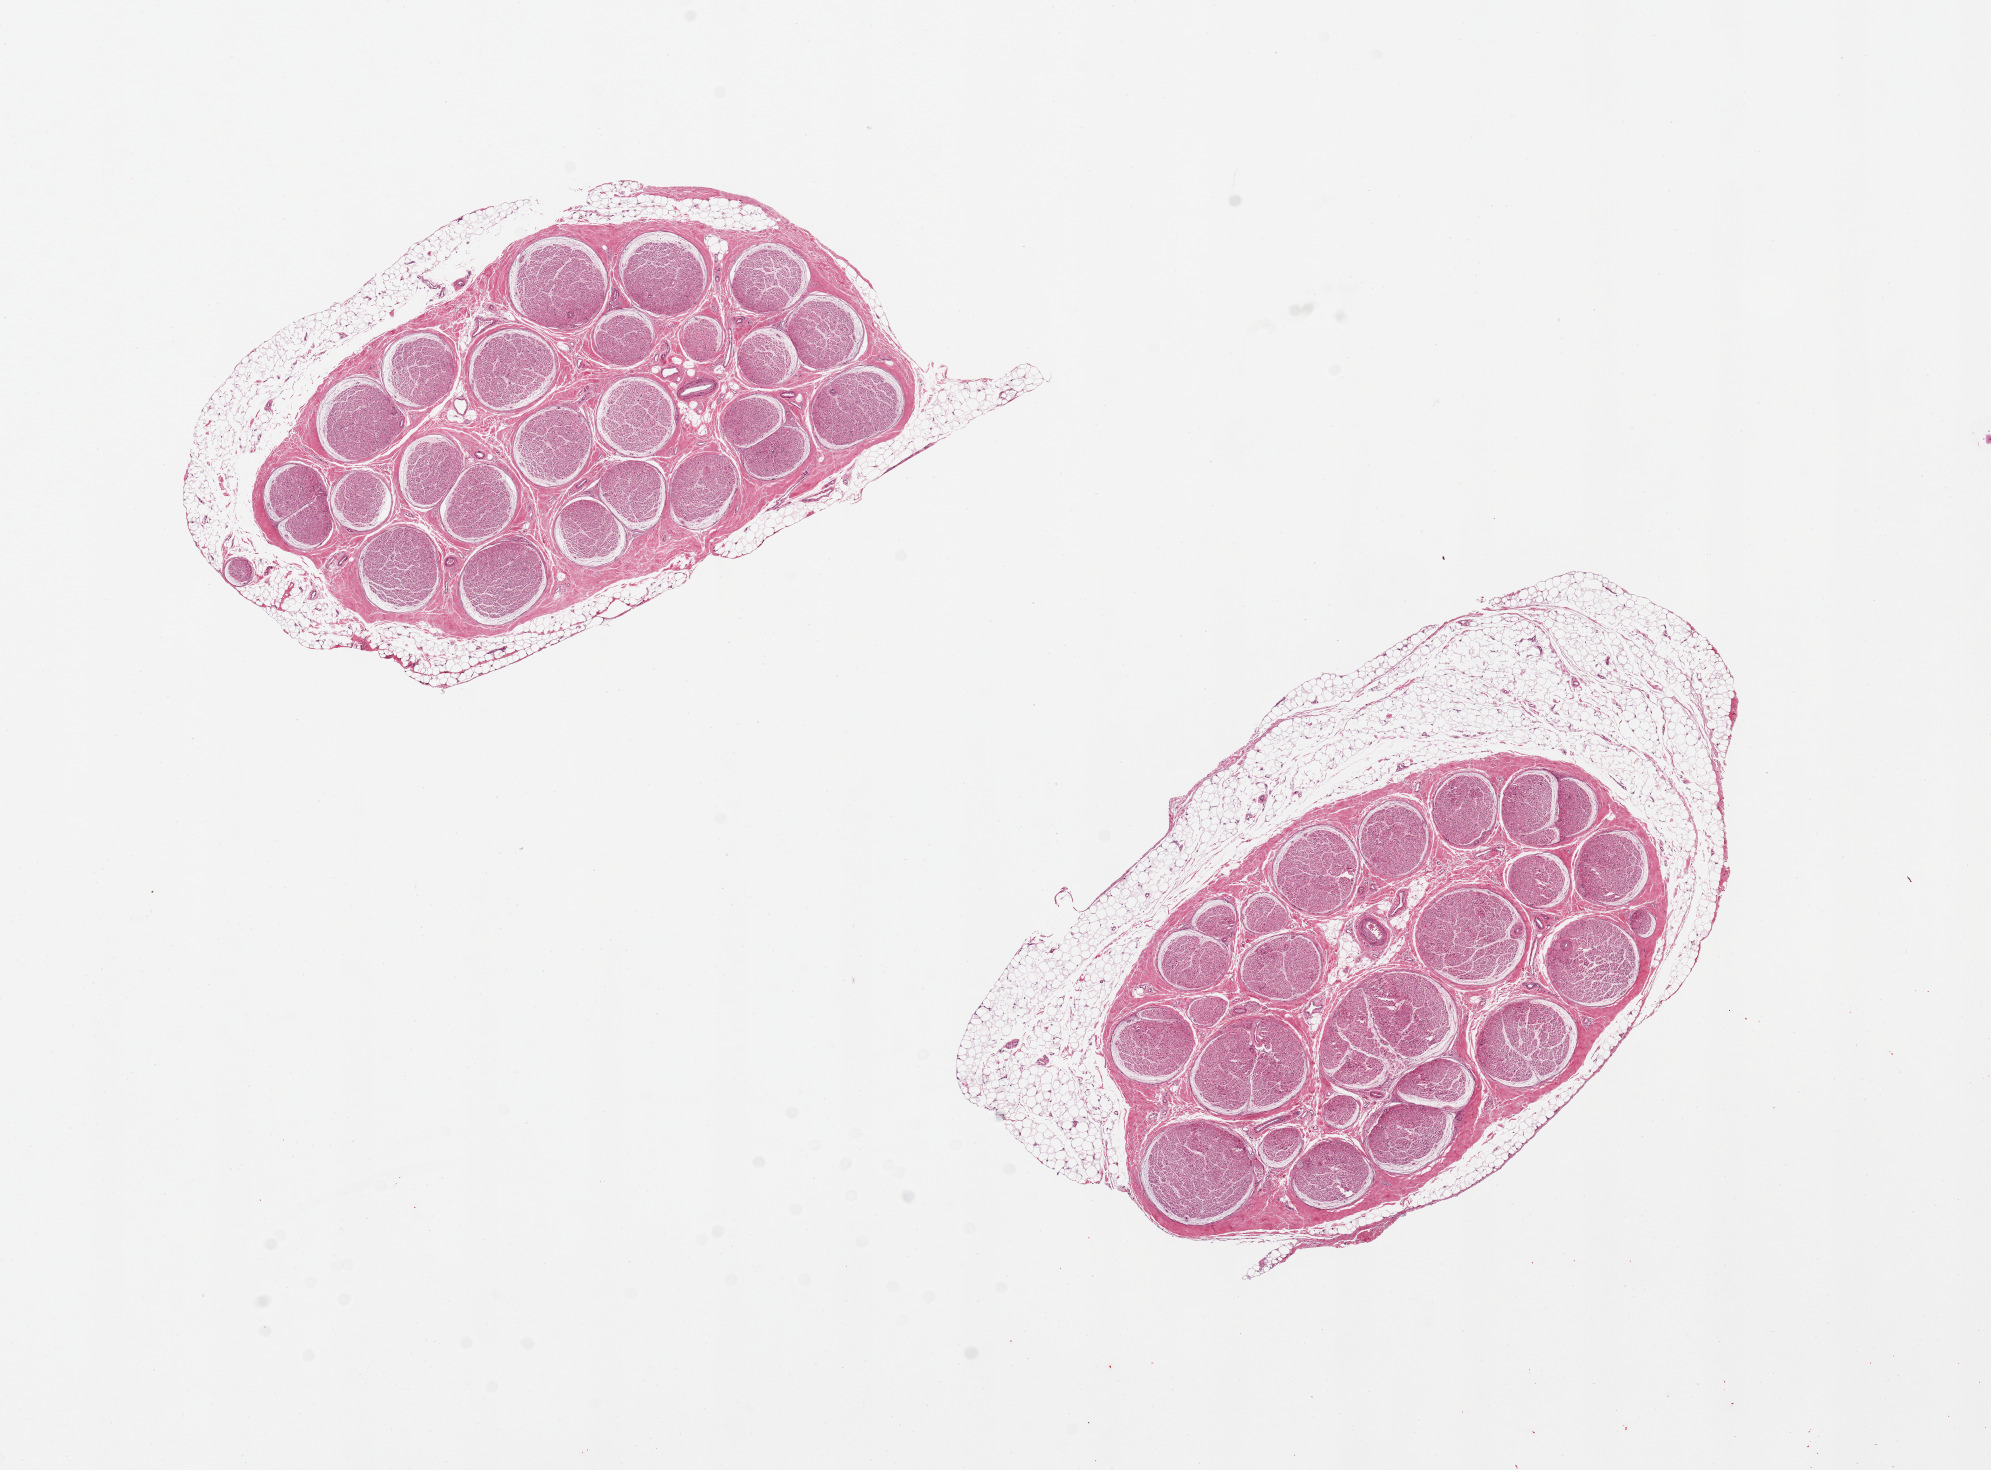
Whole-slide image, H&E stain, shown as a low-resolution overview of the whole scanned area (about 15.8 x 11.6 mm, from a 20x scan). PAXgene-fixed, paraffin-embedded tissue. Section of tibial nerve (target tissue). Tissue donor sample. Donor: male.
Review note (as recorded): 2 pieces, each with a rim of adipose tissue, up to 1.4mm in thickness on one. Fat comprises ~15% of one piece and ~35% of the other.